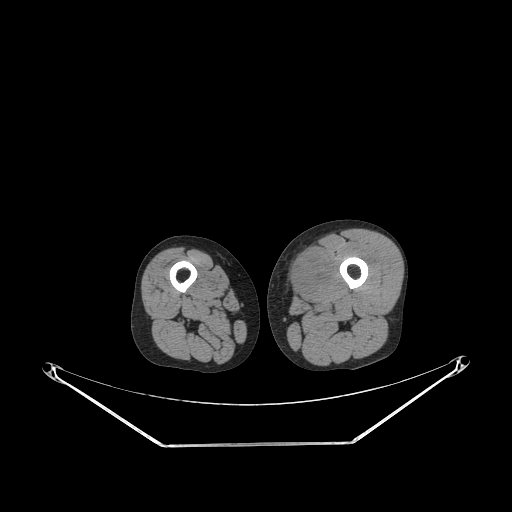
CT of an extremity soft-tissue mass (from a PET/CT study), one axial slice. Slice 222 of 267 in the series (ordered by position). Reconstruction kernel STANDARD. 140 kVp. Soft-tissue window (W 400 / L 40 HU). 512 × 512 image matrix, field of view 500 × 500 mm. Male patient. Case-level facts recorded for this patient, not image findings: histological type: pleiomorphic leiomyosarcoma; grade: high; site of the primary tumour: left thigh.
Structures marked on this image (expert contour drawn on MRI and transferred to this co-registered scan by the dataset authors):
- gross tumour volume including surrounding oedema: bounding box [x1, y1, x2, y2] px = [285, 249, 330, 296]
- gross tumour volume (mass): [285, 251, 327, 296]